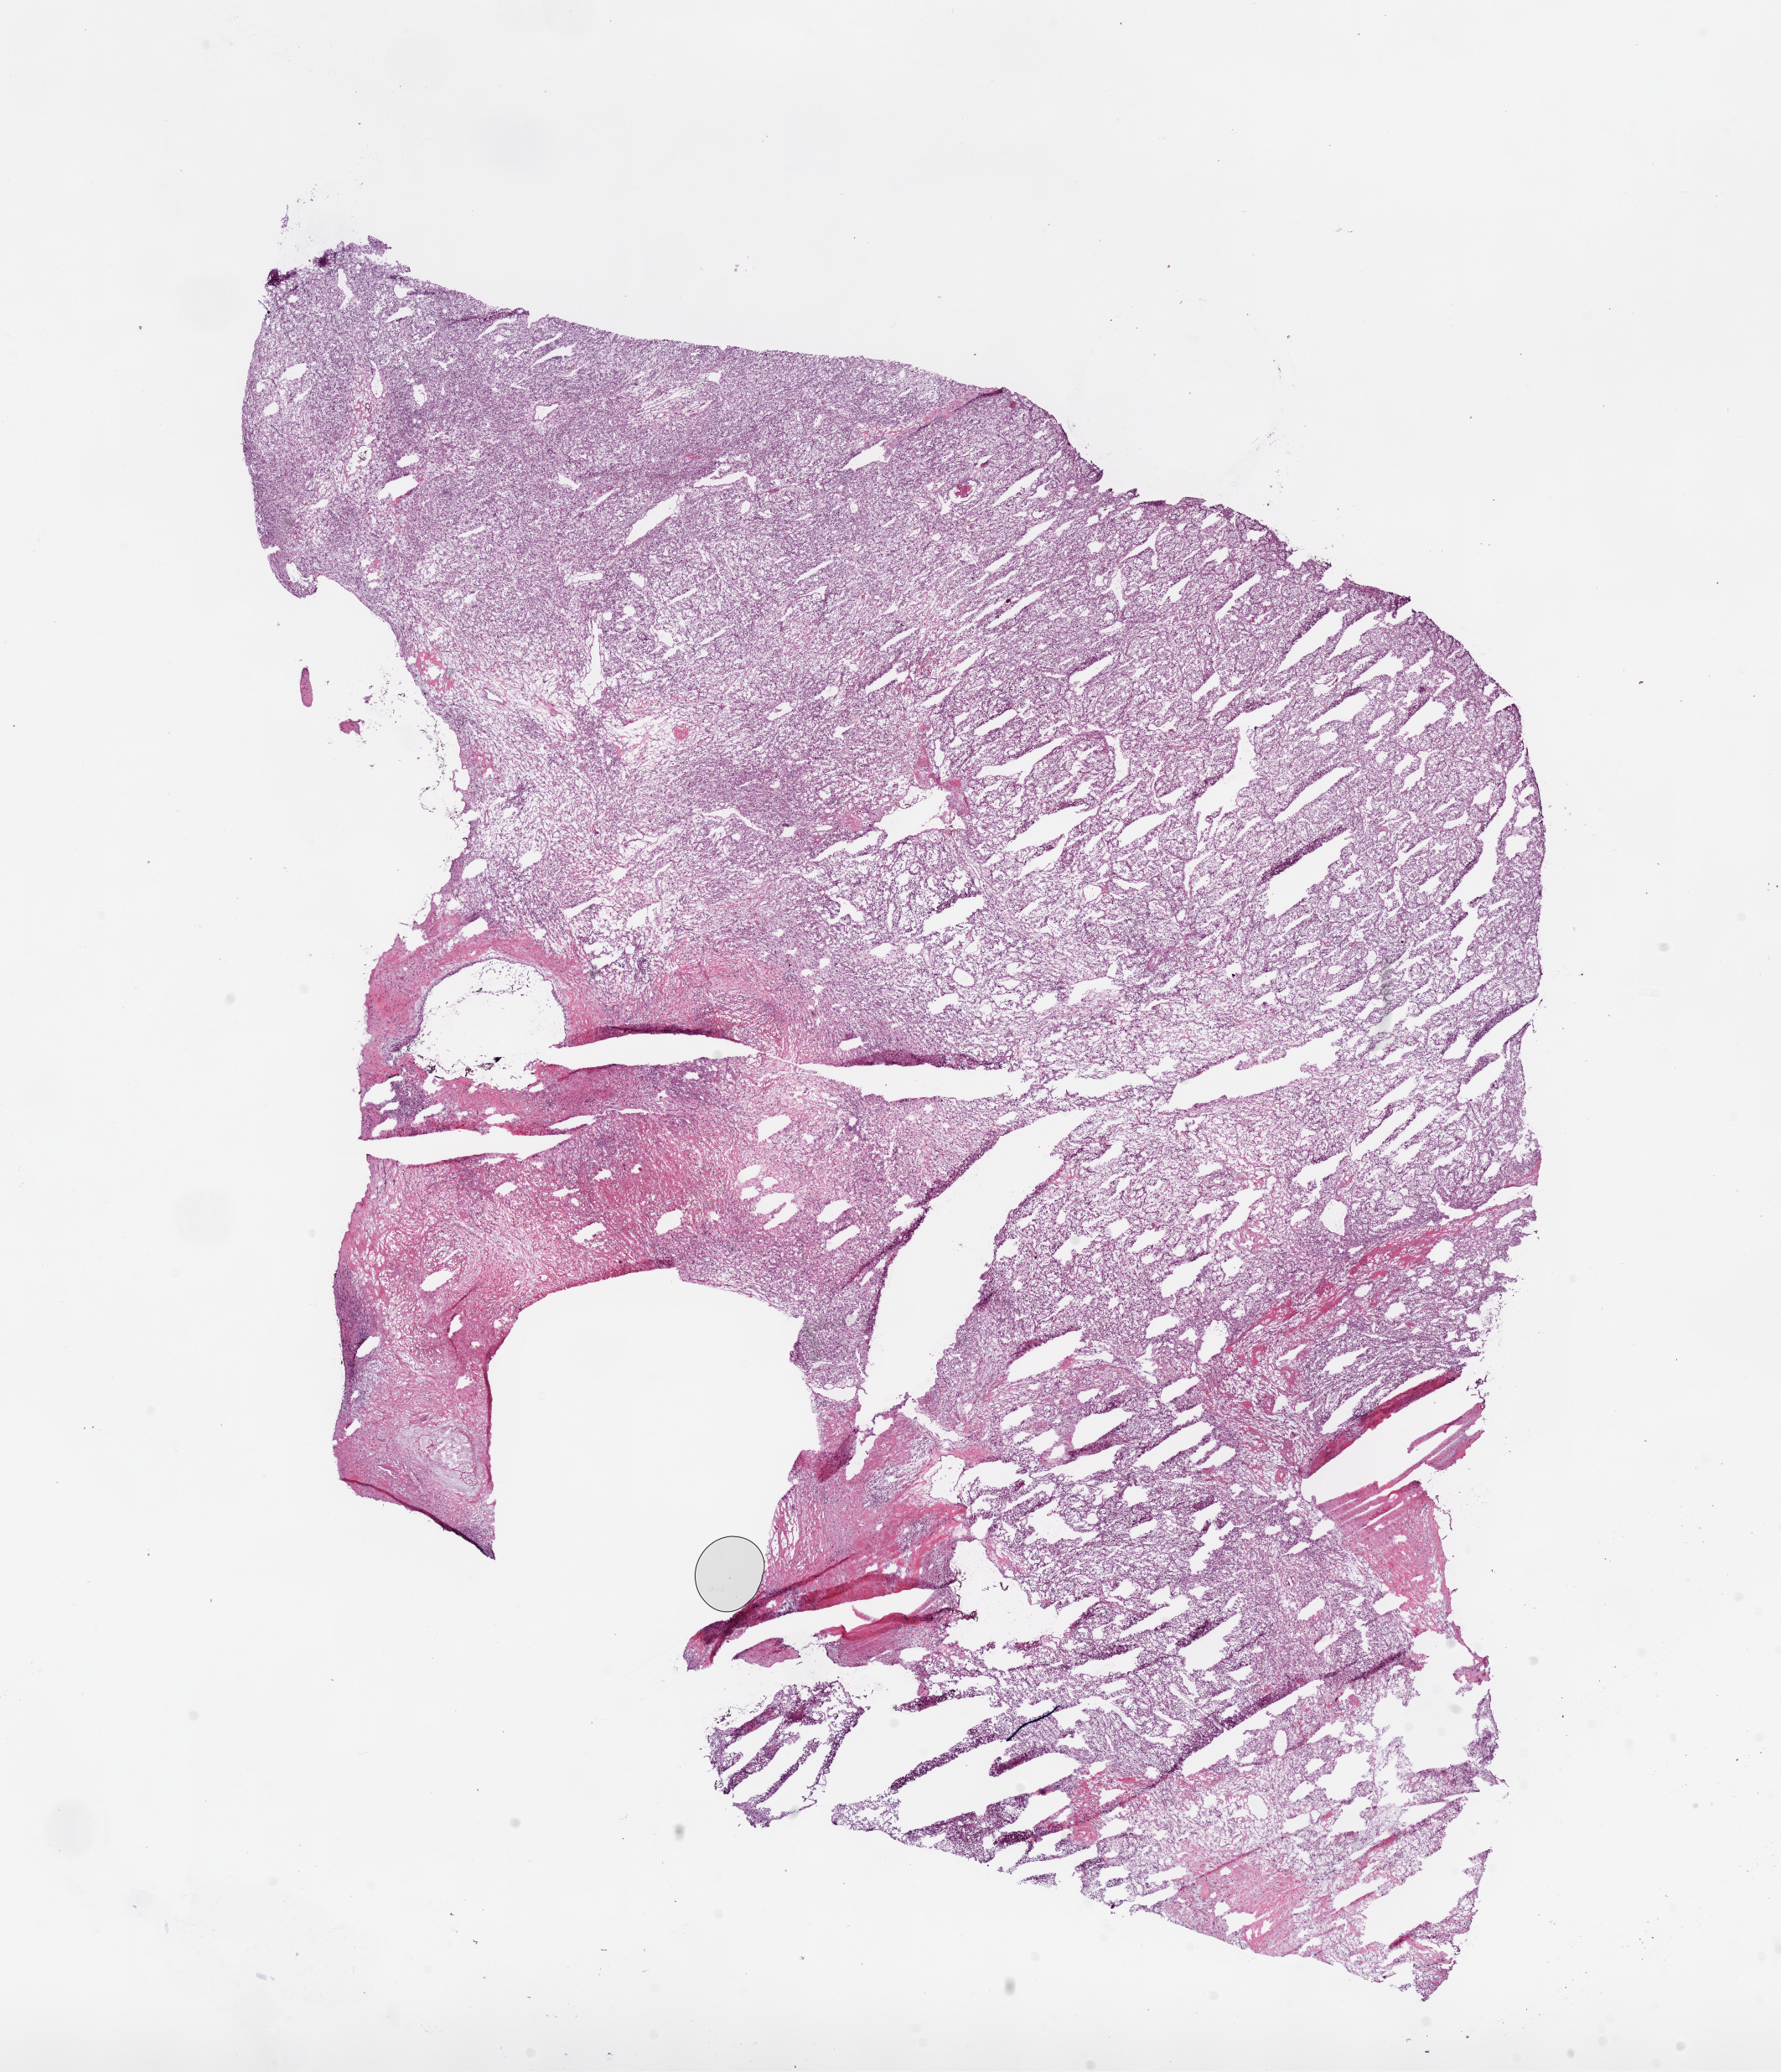
H&E-stained whole-slide image — shown as a low-resolution overview of the whole scanned area (about 17.1 x 19.8 mm, acquisition: 20x scan); frozen section; primary tumour sample from the kidney. Male patient; age at initial diagnosis 62 years. Histologic grade: G3 (poorly differentiated). Pathologist review of this section (percent, as recorded): tumour cells 85%, tumour nuclei 80%, normal cells 0%, stromal cells 15%, necrosis 0%.
AJCC pathologic stage: III. Pathologic diagnosis: Clear cell adenocarcinoma, NOS.